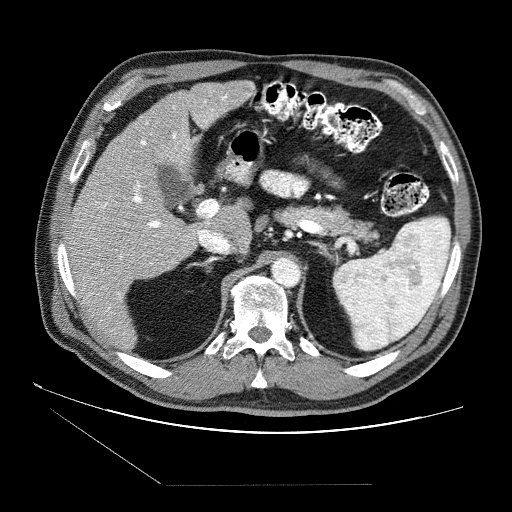
Contrast-enhanced abdominal CT (liver protocol), one axial slice; slice 46 of 87 in the series (ordered by position); 120 kVp; soft-tissue window (W 400 / L 40 HU); 2.5 mm slice thickness; 512 × 512 image matrix, field of view 400 × 400 mm. From the clinical record (not read from this slice): diagnosis: hepatocellular carcinoma (patient treated with transarterial chemoembolisation; whether this scan precedes or follows treatment is not stated here); TNM stage (as recorded): Stage-II; Child-Pugh class: B; tumour size: 2.6 cm.
Structures marked on this image (semi-automatically segmented with operator editing):
- liver parenchyma outside the tumour (the mass and vessels are separate outlines, so this box may not span the whole liver): bounding box <64,80,254,348> (left, top, right, bottom; pixels)
- liver vessels: <70,94,250,311>